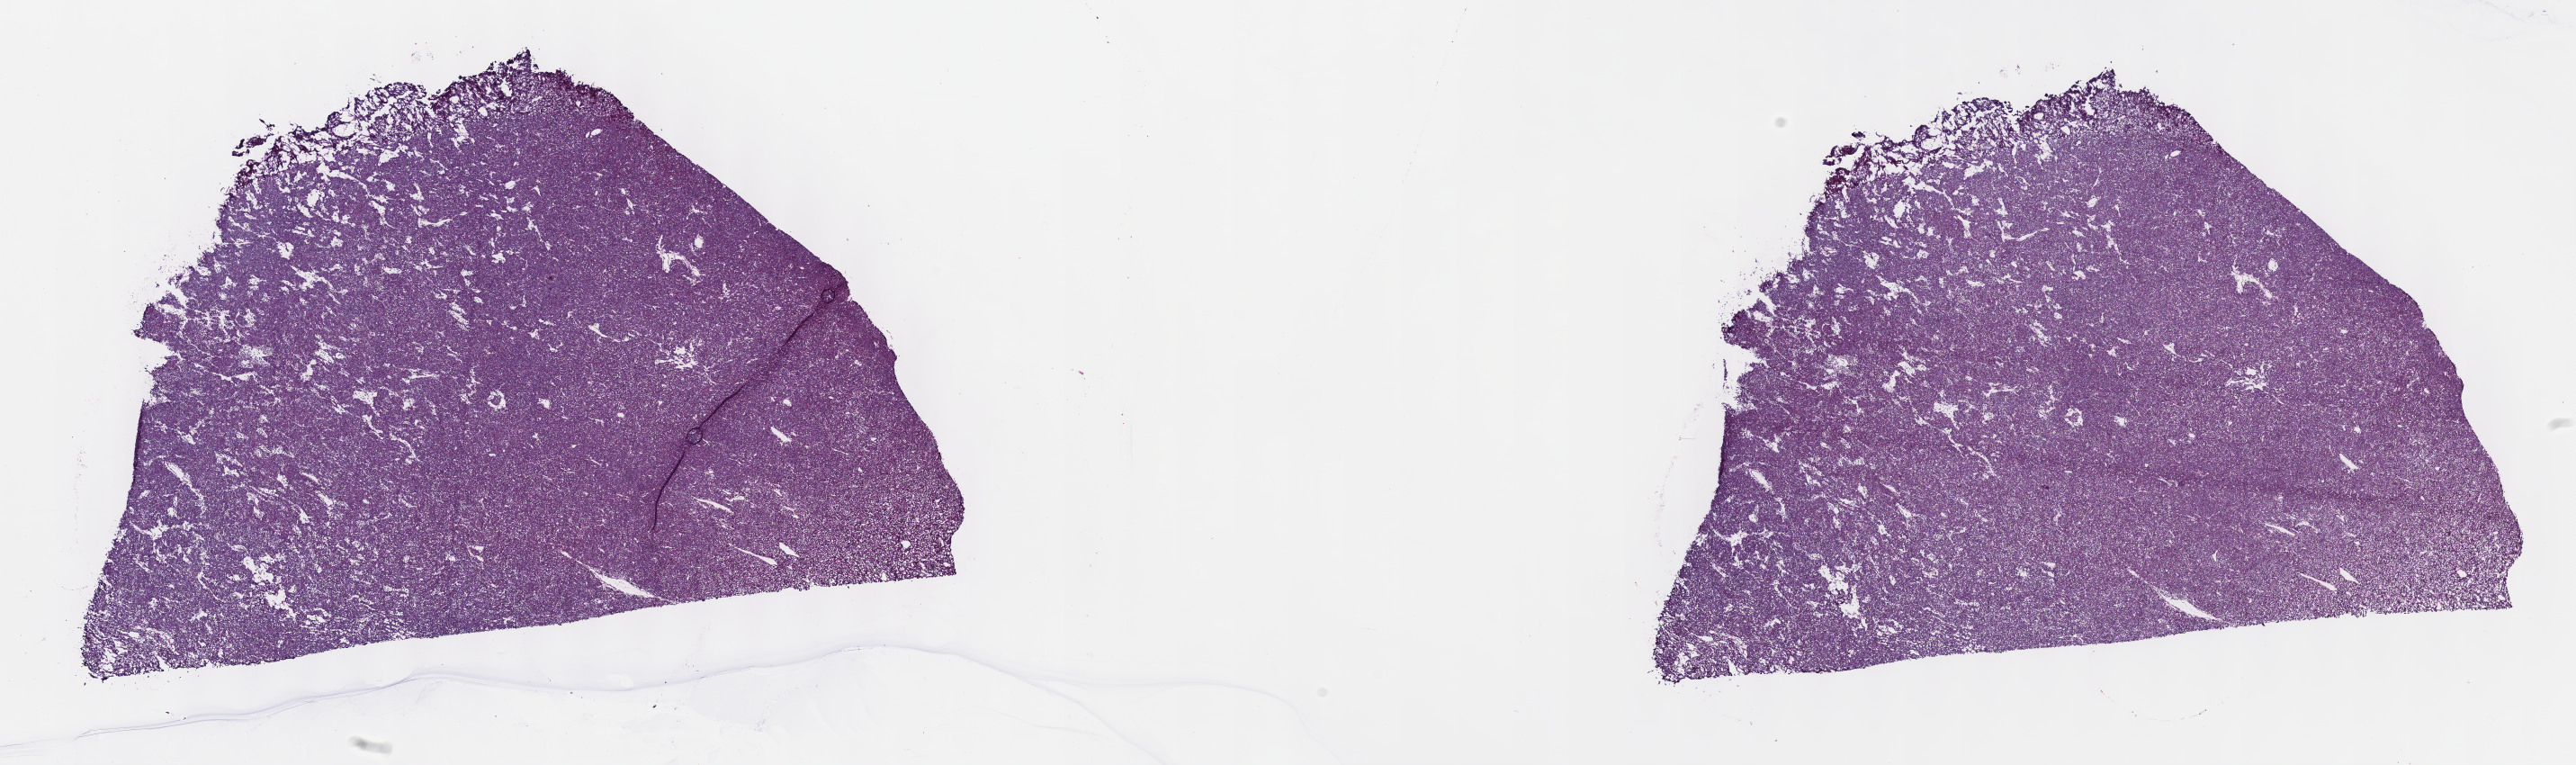
Whole-slide histology image, H&E — whole scanned area (about 23.2 x 6.9 mm) shown as a low-resolution overview; frozen section; sample: primary tumour, thymus. Male patient; age at initial diagnosis 67 years. Composition of this section per pathologist review: tumour cells 100%, tumour nuclei 80%, normal cells 0%, stromal cells 0%, necrosis 0%. Infiltration values recorded for this section: lymphocyte infiltration 1%, monocyte infiltration 0%, neutrophil infiltration 0%.
Pathologic diagnosis: Thymoma, type A, NOS.